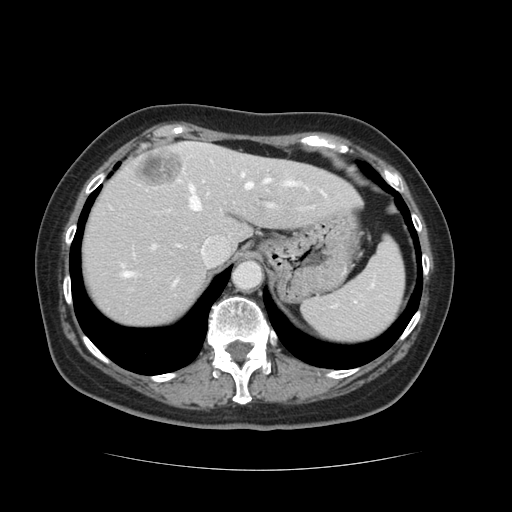
Contrast-enhanced abdominal CT, one axial slice. Position 98 of 128 along the scan axis. Intravenous contrast given. Soft-tissue window (W 400 / L 40 HU). 2.5 mm slice thickness. 512 × 512 image matrix. Female patient, age 67 years. From the clinical record (not read from this slice): diagnosis: colorectal cancer liver metastases, imaged before liver resection; multiple liver metastases: yes; largest metastasis: 3 cm; disease in both lobes: yes.
Structures marked on this image (manually delineated by an expert):
- hepatic veins: bounding box <122,173,299,287> (left, top, right, bottom; pixels)
- liver: <81,143,359,328>
- planned liver remnant (the part of the liver to remain after resection): <81,154,359,328>
- portal vein (with intrahepatic branches): <153,159,276,248>
- liver metastasis: <135,150,182,187>